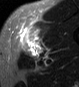
MRI of an extremity soft-tissue mass, one axial slice. Slice 33 of 45 in the series (ordered by position). STIR. MR volume resampled by the dataset authors to the PET/CT grid (not the native acquisition matrix). 3.27 mm slice thickness. 79 × 87 image matrix, field of view 77 × 85 mm. Male patient. Case-level facts recorded for this patient, not image findings: histological type: pleiomorphic leiomyosarcoma; grade: high; site of the primary tumour: left thigh.
Annotated regions visible in this slice (expert contour drawn on MRI and transferred to this co-registered scan by the dataset authors):
- gross tumour volume including surrounding oedema: box from (x=20, y=23) to (x=44, y=58) px
- gross tumour volume (mass): (x=25, y=39)–(x=41, y=56)